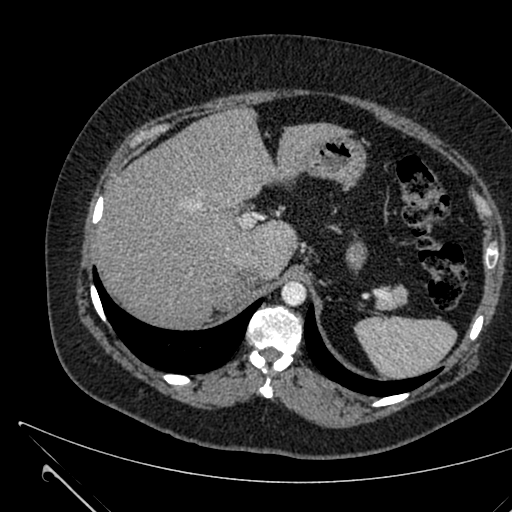
Contrast-enhanced abdominal CT, one axial slice; 120 kVp; intravenous contrast given; soft-tissue window (W 400 / L 40 HU); 512 × 512 image matrix, field of view 376 × 376 mm. Female patient, age 36 years. Case-level facts recorded for this patient, not image findings: diagnosis: adrenocortical carcinoma; tumour side: right adrenal; tumour size at pathology: 10 cm; Ki-67 index: 20 %; stage (as recorded): 4.
Outlined on this slice (semi-automatically segmented with operator editing):
- mass: box from (x=215, y=282) to (x=244, y=310) px